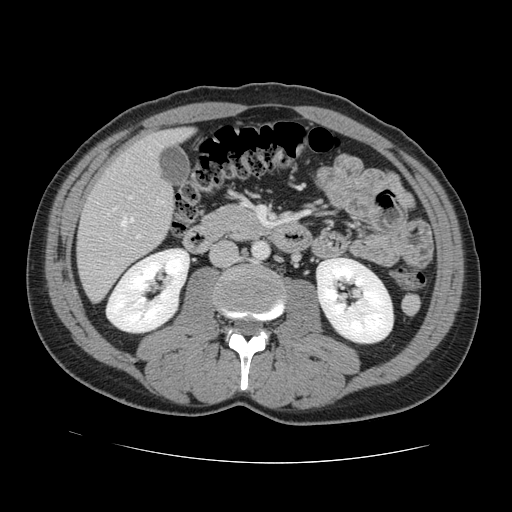
Contrast-enhanced abdominal CT, one axial slice. Slice 46 of 131 in the series (ordered by position). 120 kVp. Intravenous contrast given. Soft-tissue window (W 400 / L 40 HU). 2.5 mm slice thickness. 512 × 512 image matrix. Male patient, age 40 years. From the clinical record (not read from this slice): diagnosis: colorectal cancer liver metastases, imaged before liver resection; multiple liver metastases: yes; largest metastasis: 2.9 cm; disease in both lobes: yes.
Outlined on this slice (outlined manually by an expert reader):
- hepatic veins: bounding box (x1, y1, x2, y2) in pixels: (121, 217, 133, 227)
- liver: (78, 130, 189, 300)
- planned liver remnant (the part of the liver to remain after resection): (126, 129, 190, 166)
- portal vein (with intrahepatic branches): (129, 196, 141, 238)